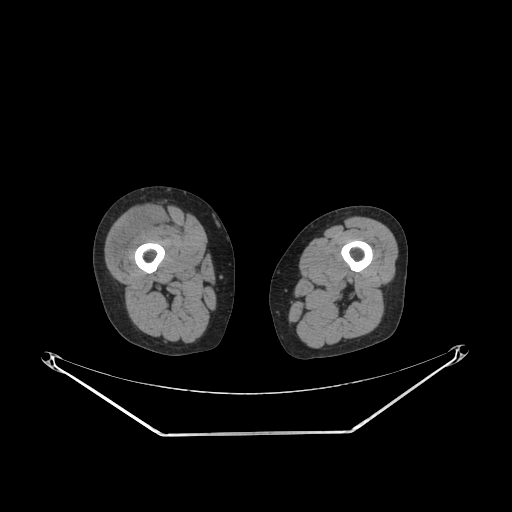
CT of an extremity soft-tissue mass (from a PET/CT study), one axial slice. Position 216 of 311 along the scan axis. Reconstruction kernel SOFT. 140 kVp. Soft-tissue window (W 400 / L 40 HU). 3.75 mm slice thickness. 512 × 512 image matrix, field of view 500 × 500 mm. Female patient. From the clinical record (not read from this slice): histological type: pleiomorphic undifferentiated sarcoma; grade: high; site of the primary tumour: right quadricep.
Annotated regions visible in this slice (expert contour drawn on MRI and transferred to this co-registered scan by the dataset authors):
- tumour plus oedema (research contour): bounding box <109,210,163,264> (left, top, right, bottom; pixels)